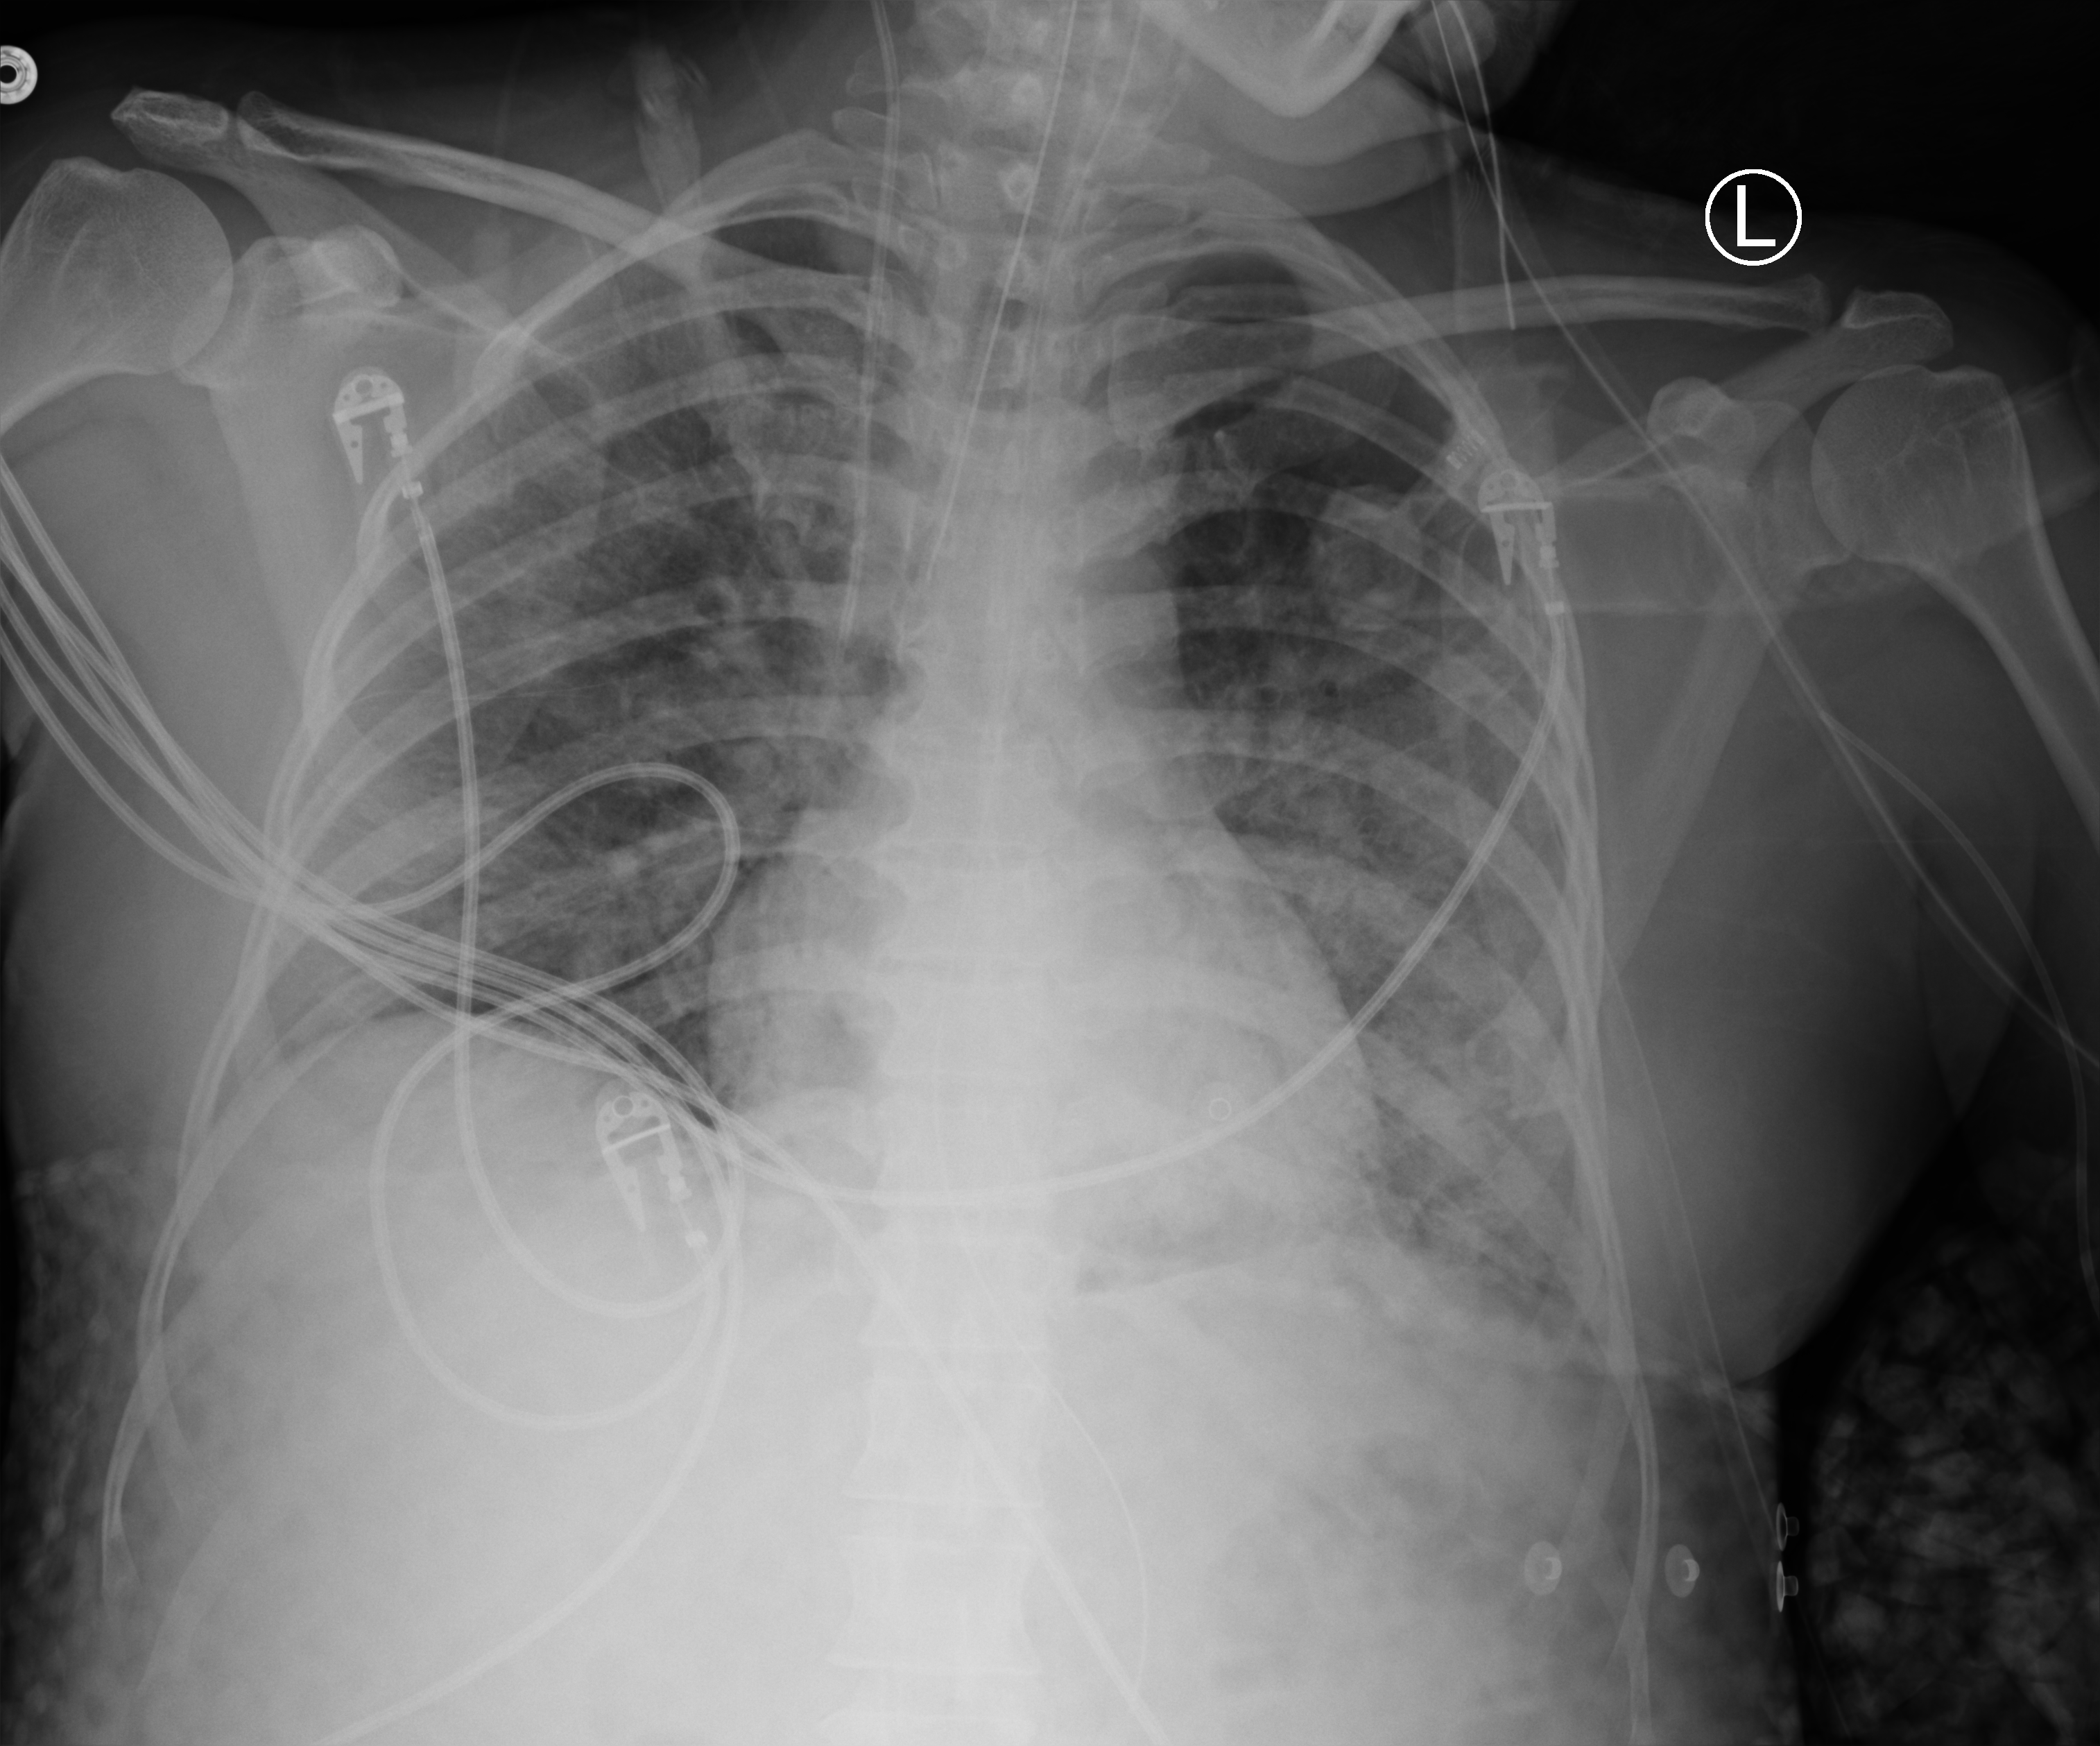
Portable chest radiograph. Patient hospitalised with COVID-19; female, aged 18–59 years.
From the hospital-stay record, not from the radiograph (when in the stay this image was taken is not recorded): admitted to intensive care during this hospital stay: yes.